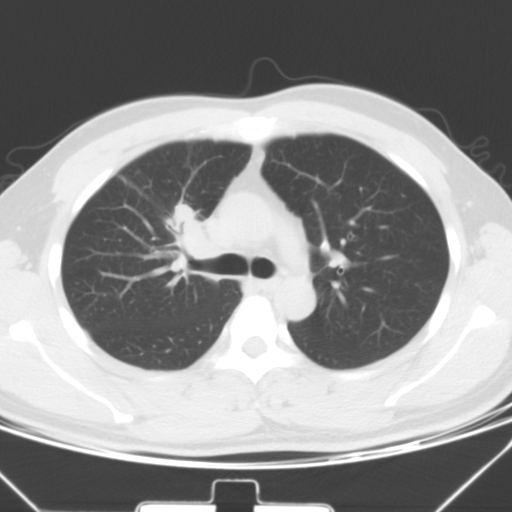
Chest CT, one axial slice; position 40 of 60 along the scan axis; lung window (W 1500 / L -600 HU); 5 mm slice thickness; 512 × 512 image matrix. Patient: male, 35 years. Case-level facts recorded for this patient, not image findings: clinical TNM (as recorded): T1c N1 M1b.
Outlined on this slice (rectangle marked by the reading radiologist):
- lung tumour (recorded histology: adenocarcinoma): bounding box (x1, y1, x2, y2) in pixels: (169, 200, 223, 265)